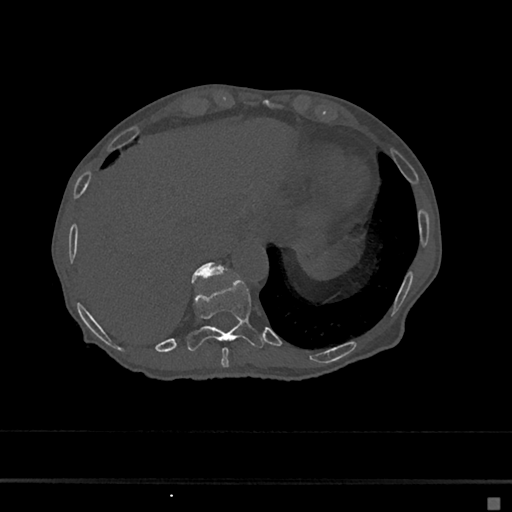
CT including the spine, one axial slice. Position 226 of 797 along the scan axis. 120 kVp. Bone window (W 1800 / L 400 HU). 0.5 mm slice thickness. 512 × 512 image matrix, field of view 360 × 360 mm. Patient: female, 68 years. Case-level facts recorded for this patient, not image findings: primary cancer: renal.
Structures marked on this image (semi-automatic segmentation, software-assisted and operator-edited):
- T10 vertebra: box from (x=187, y=279) to (x=264, y=351) px
- T11 vertebra: (x=192, y=262)–(x=225, y=280)
- T9 vertebra: (x=221, y=347)–(x=229, y=367)